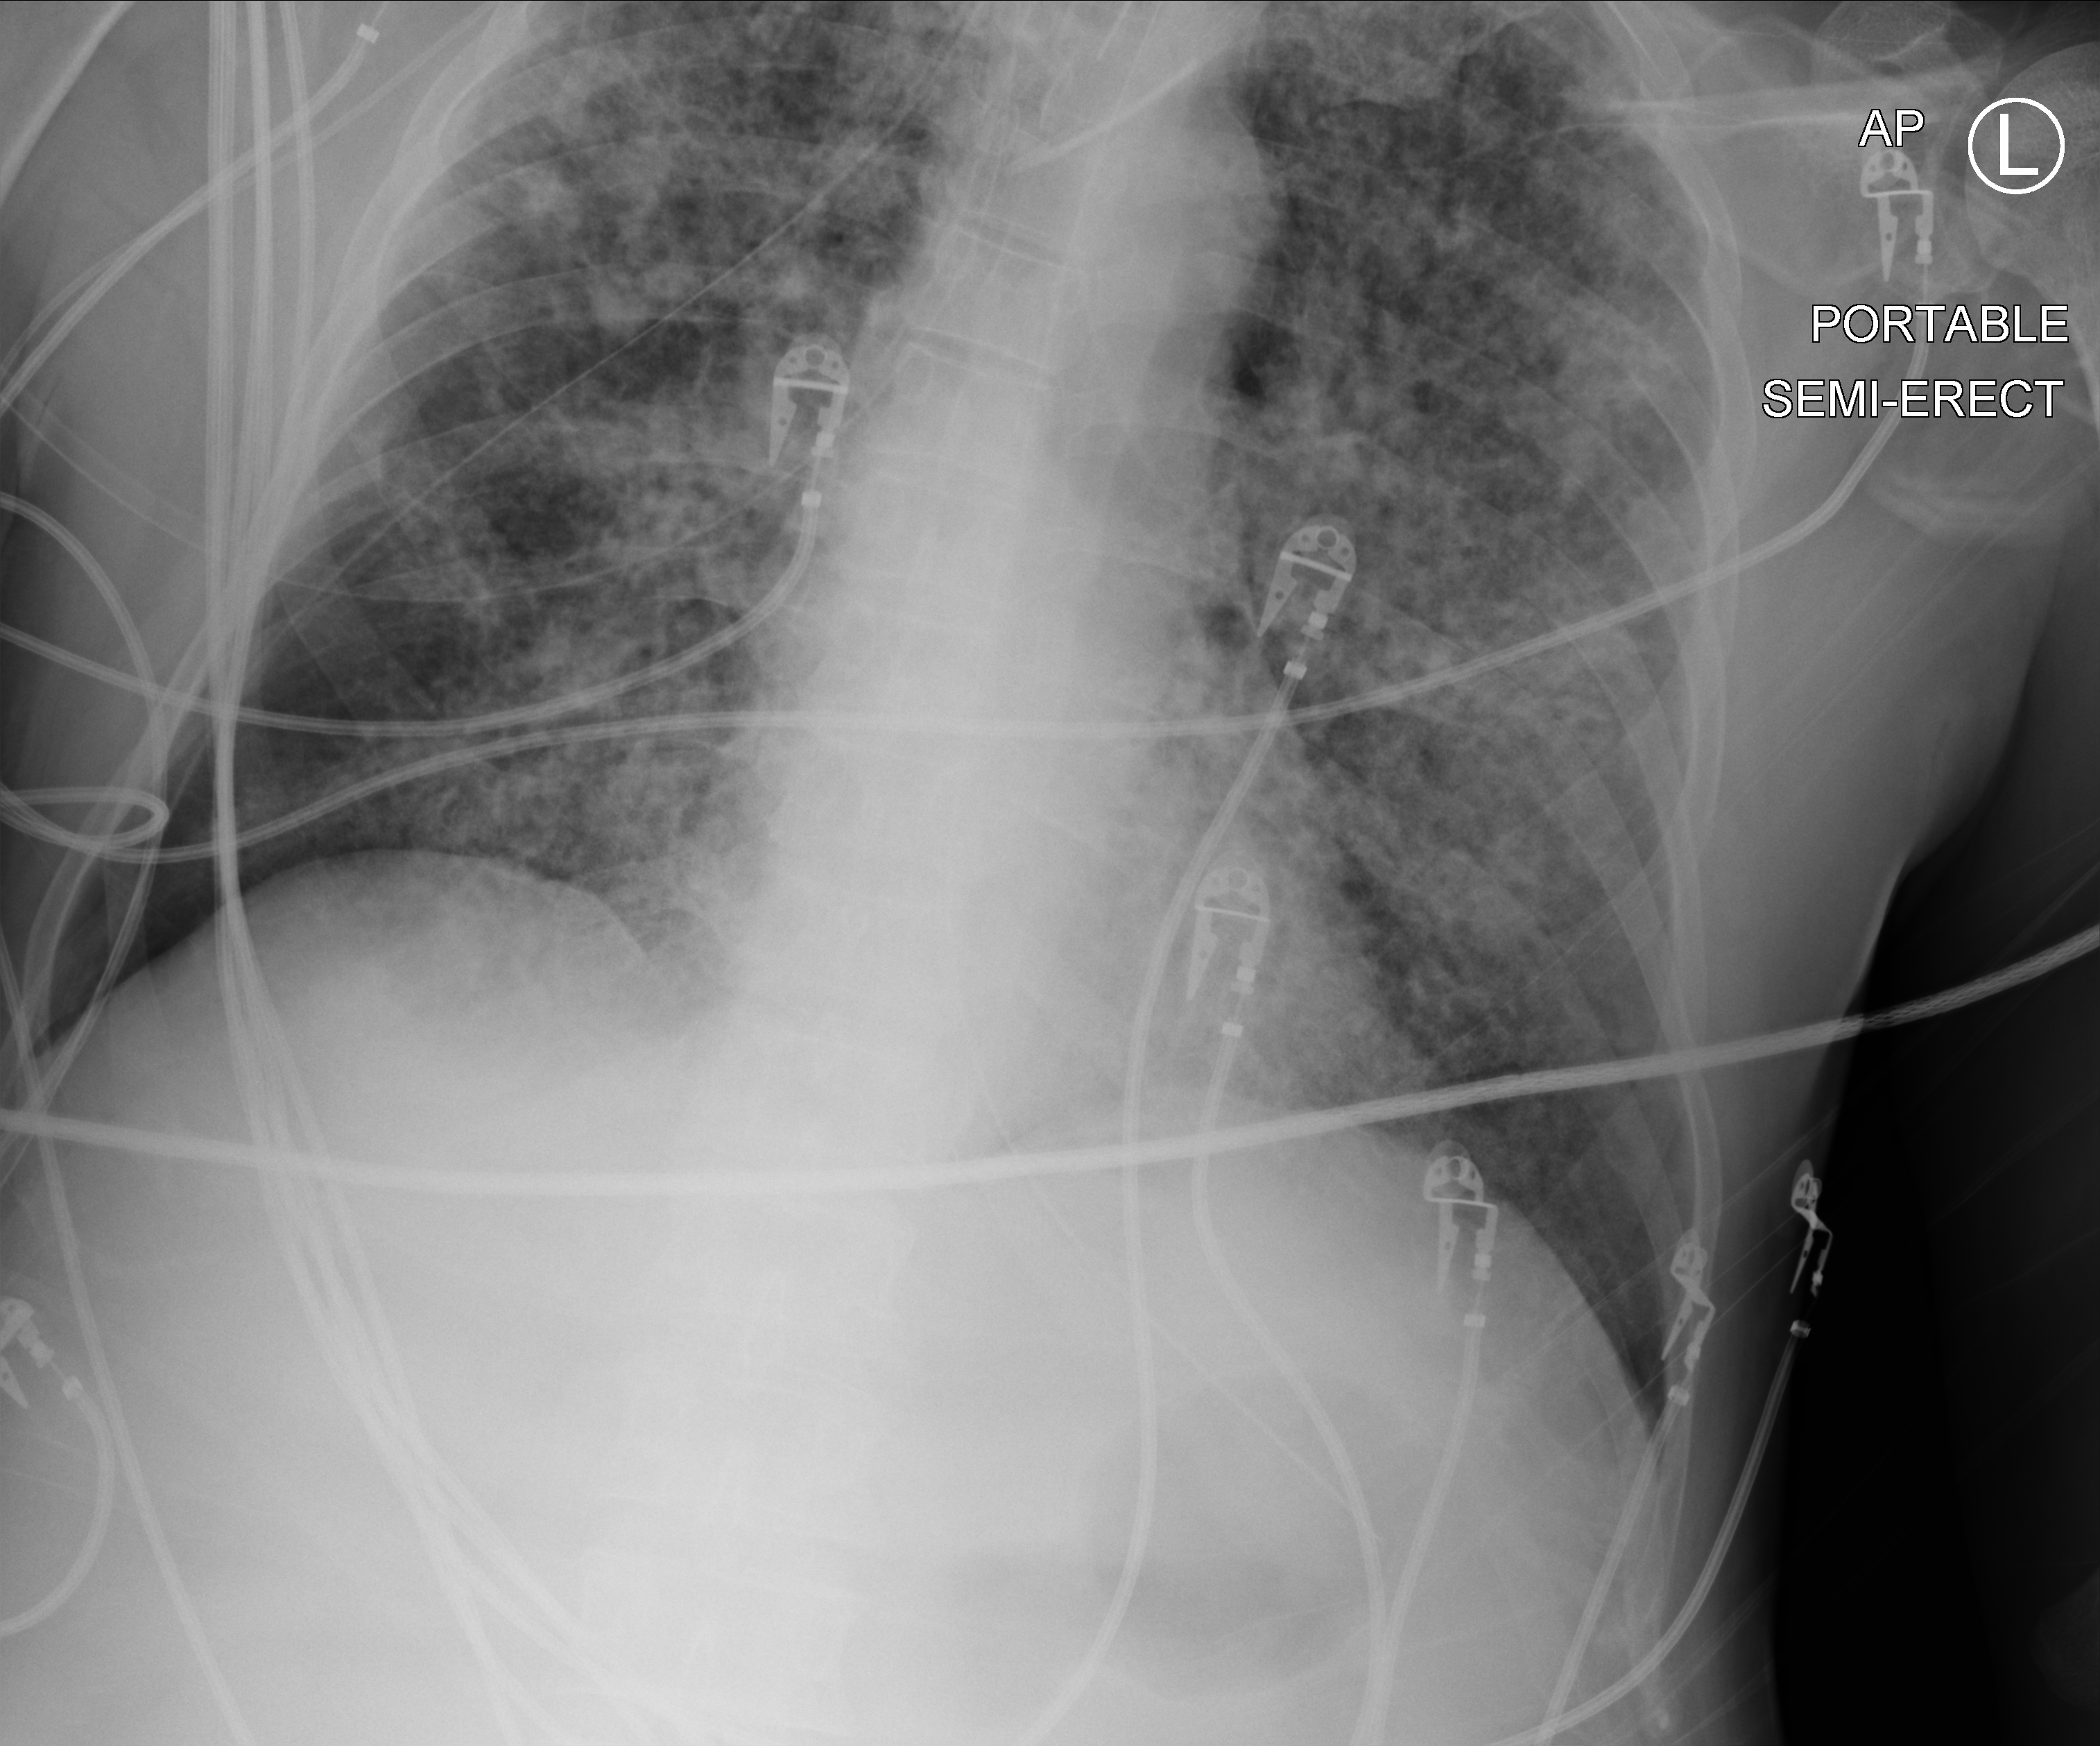
Bedside chest radiograph (computed radiography); anteroposterior (AP) projection. Patient hospitalised with COVID-19; male, aged 60–74 years.
Admission-level facts for this patient (not findings on this image; timing relative to this image not recorded): admitted to intensive care during this hospital stay: yes.